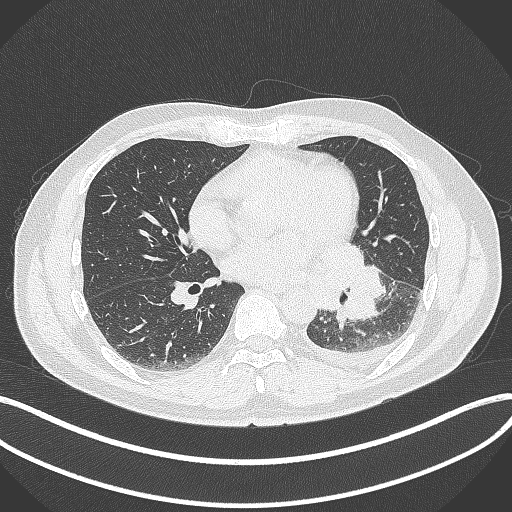
Chest CT, one axial slice; slice 162 of 342 in the series (ordered by position); reconstruction kernel B70f; 120 kVp; lung window (W 1500 / L -600 HU); 1 mm slice thickness; 512 × 512 image matrix, field of view 400 × 400 mm. Patient: male, 58 years. Case-level facts recorded for this patient, not image findings: clinical TNM (as recorded): T3 N1 M1b.
Outlined on this slice (bounding box drawn by a radiologist):
- lung tumour (recorded histology: small cell carcinoma): bounding box <316,239,386,327> (left, top, right, bottom; pixels)